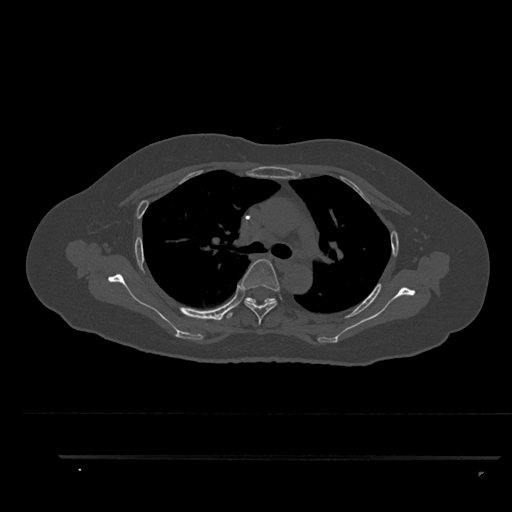
CT including the spine, one axial slice. Slice 631 of 797 in the series (ordered by position). Reconstruction kernel Br40s/3. 120 kVp. Bone window (W 1800 / L 400 HU). 0.5 mm slice thickness. 512 × 512 image matrix, field of view 408 × 408 mm. Female patient, age 44 years. Case-level facts recorded for this patient, not image findings: primary cancer: renal.
Annotated regions visible in this slice (semi-automatic segmentation, software-assisted and operator-edited):
- T4 vertebra: bounding box [x1, y1, x2, y2] px = [240, 259, 280, 325]
- T5 vertebra: [226, 297, 275, 319]